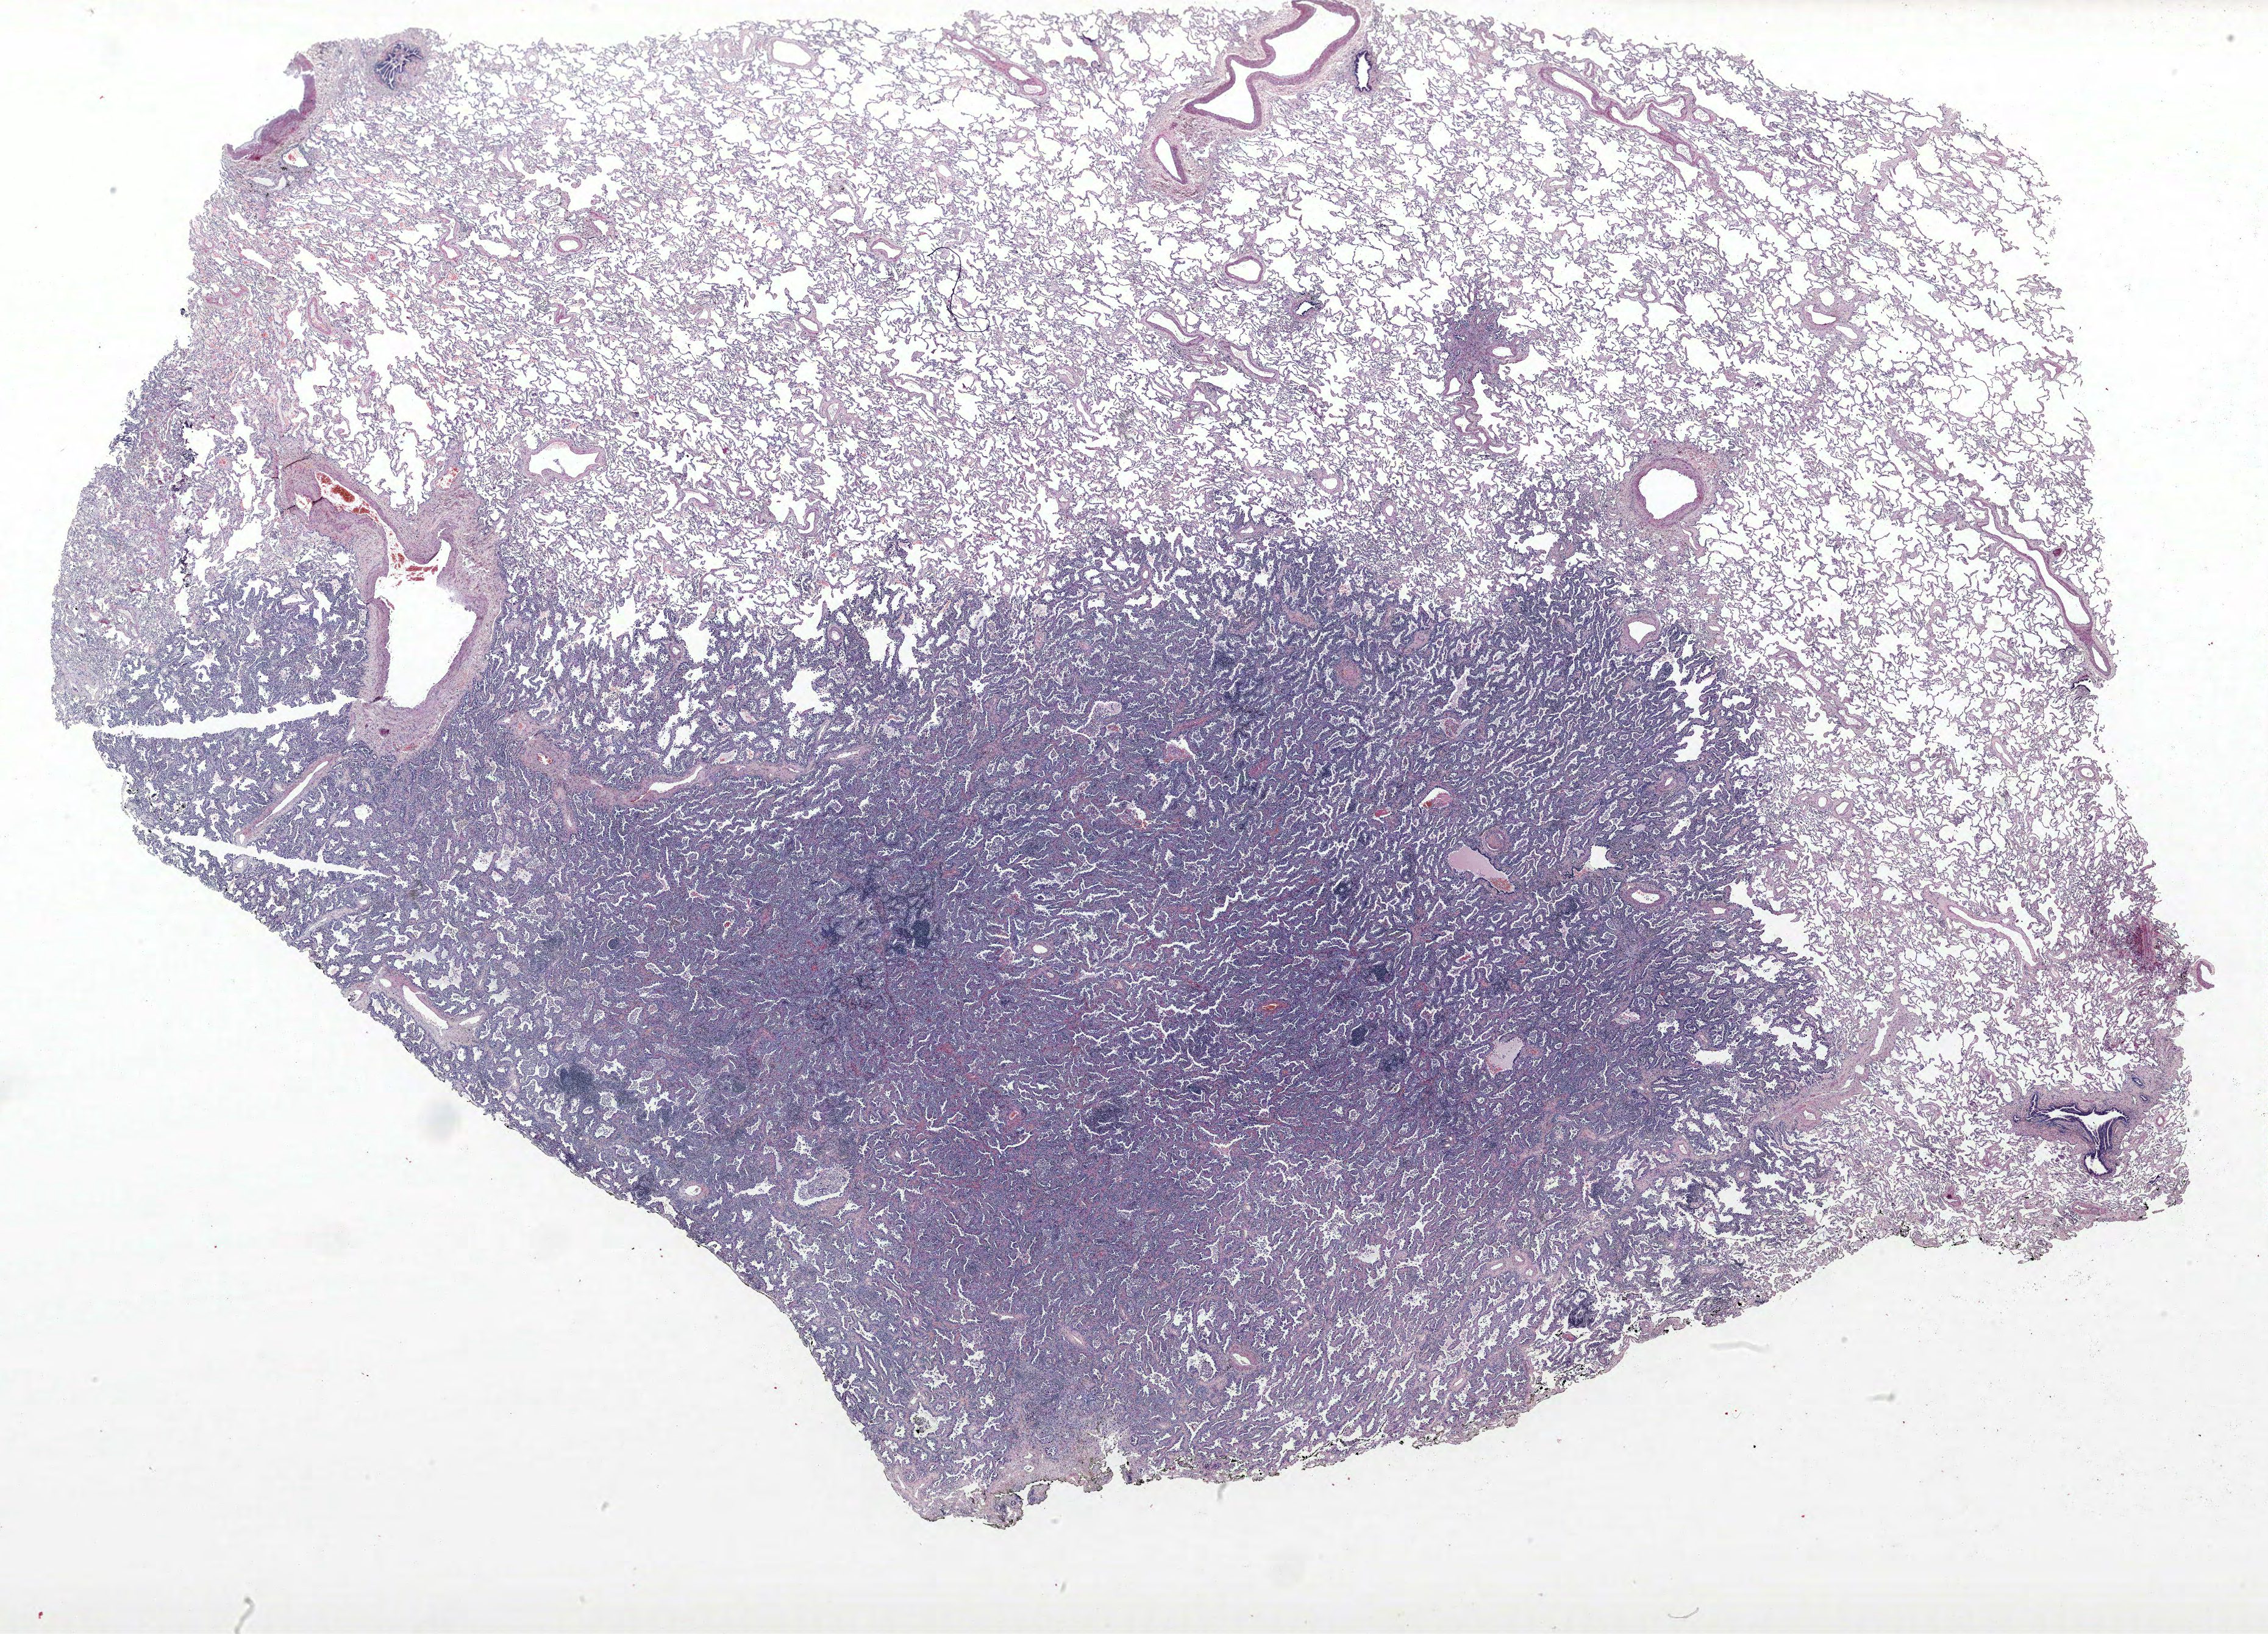
H&E whole-slide image, a low-resolution overview of the entire scanned area, about 29.8 x 21.4 mm (acquisition: 40x scan). FFPE section. Lung. Male patient, aged 71 at enrolment. Former smoker at enrolment.
Participant's lung-cancer diagnosis: Bronchiolo-alveolar adenocarcinoma, NOS.